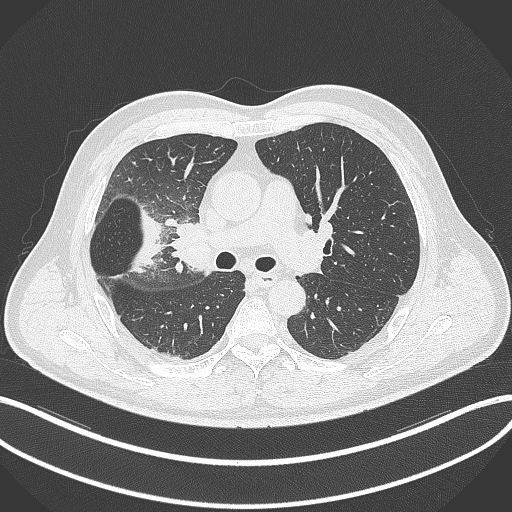
Chest CT, one axial slice; position 200 of 348 along the scan axis; reconstruction kernel B70f; 120 kVp; lung window (W 1500 / L -600 HU); 1 mm slice thickness; 512 × 512 image matrix, field of view 400 × 400 mm. Patient: male, 55 years. Case-level facts recorded for this patient, not image findings: clinical TNM (as recorded): T3 N2 M1.
Structures marked on this image (bounding box drawn by a radiologist):
- lung tumour (recorded histology: adenocarcinoma): bounding box [x1, y1, x2, y2] px = [125, 200, 166, 275]